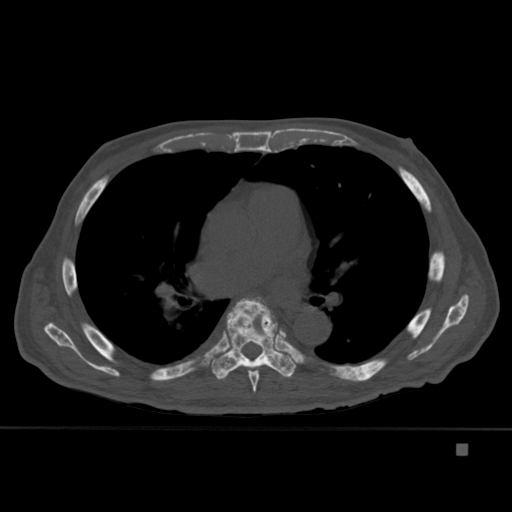
CT including the spine, one axial slice. Slice 284 of 451 in the series (ordered by position). Bone window (W 1800 / L 400 HU). 512 × 512 image matrix, field of view 378 × 378 mm. Patient: male, 75 years. Case-level facts recorded for this patient, not image findings: primary cancer: prostate.
Outlined on this slice (semi-automatically segmented with operator editing):
- T4 vertebra: bounding box [x1, y1, x2, y2] px = [271, 322, 286, 341]
- T6 vertebra: [248, 297, 273, 393]
- T7 vertebra: [211, 298, 296, 380]